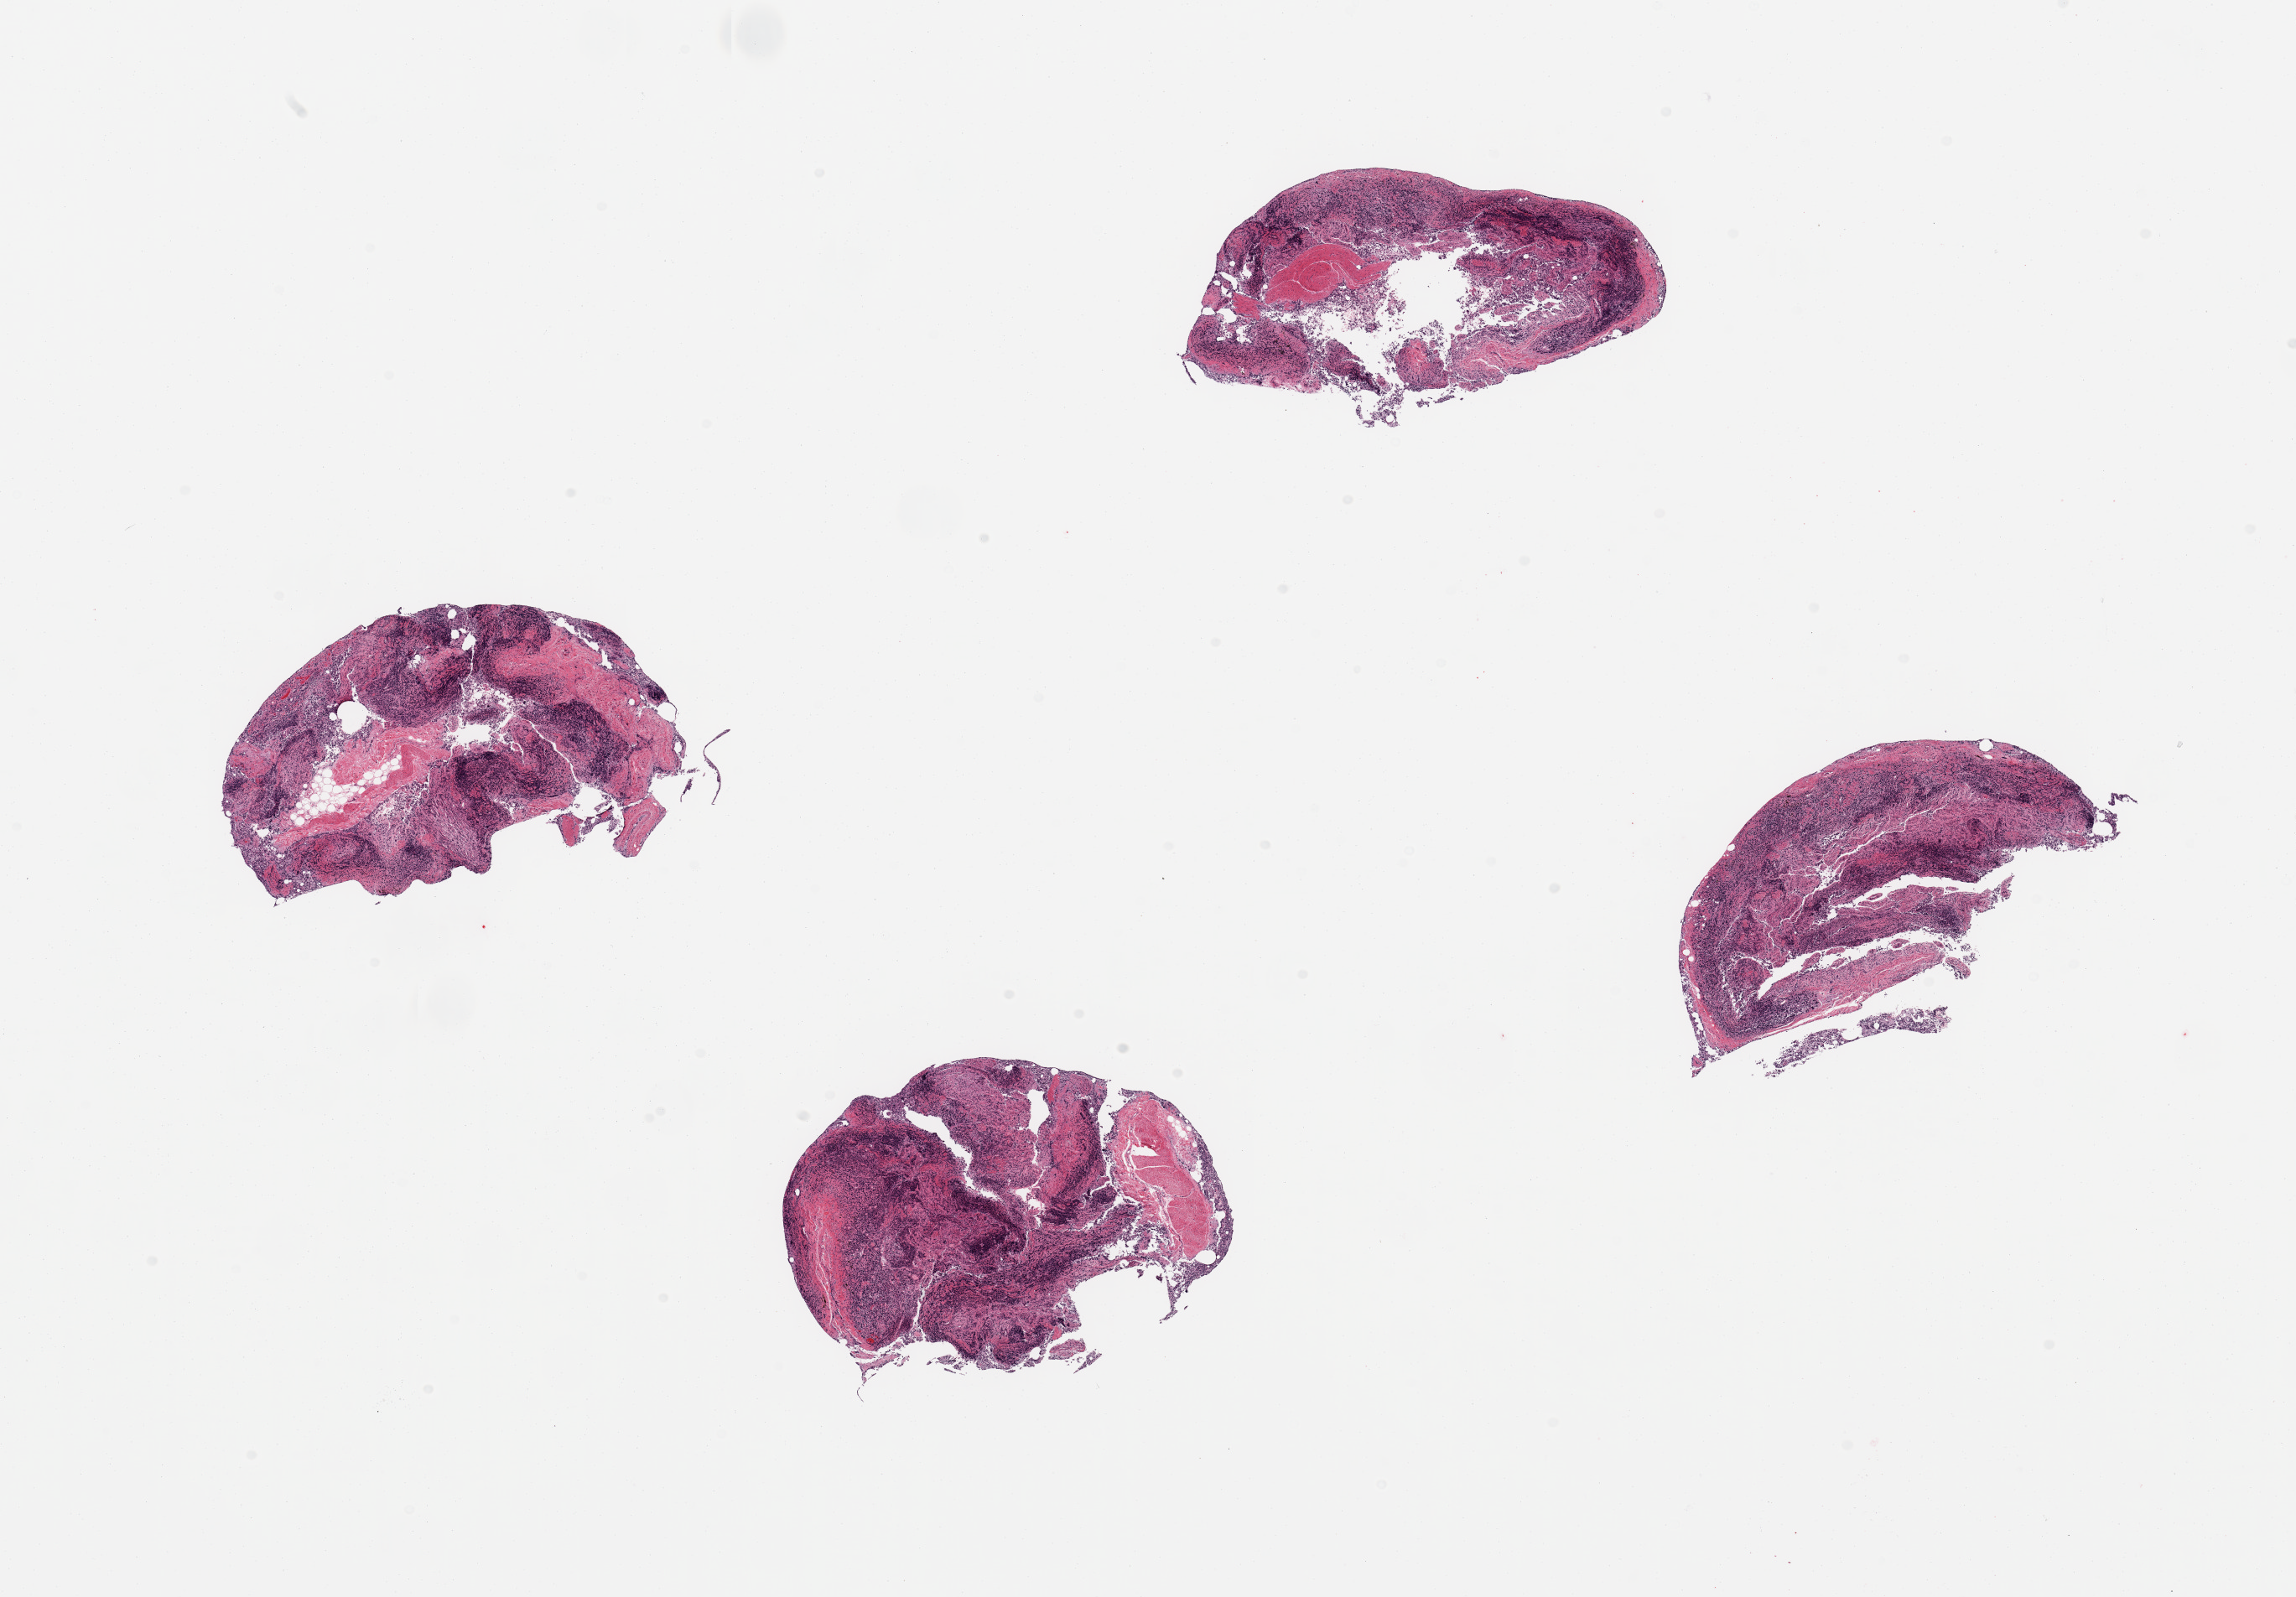
Whole-slide image, H&E stain — a low-resolution overview of the entire scanned area, about 21.7 x 15.1 mm (from a 20x scan); PAXgene-fixed paraffin-embedded (PFPE) section; sampled site (target tissue): ileum; donor tissue sample. Male donor.
Pathologist's review note for this sample: 4 pieces,glandular elements autolyzed; target lymphoid aggregates are ~20-30% of tissue.